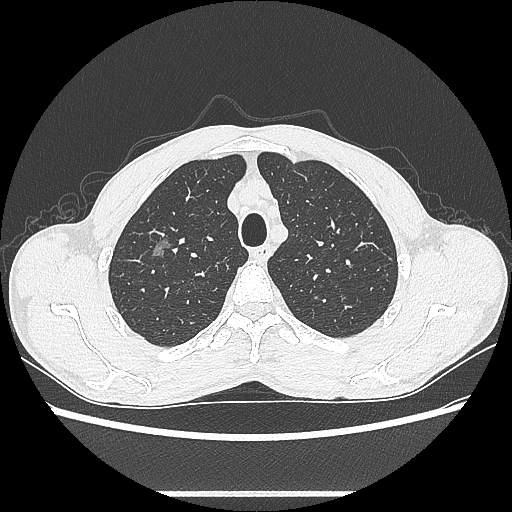
Chest CT, one axial slice. Slice 479 of 601 in the series (ordered by position). 100 kVp. Lung window (W 1500 / L -600 HU). 0.62 mm slice thickness. 512 × 512 image matrix. Male patient, age 54 years. Case-level facts recorded for this patient, not image findings: clinical TNM (as recorded): T1a N0 M0.
Outlined on this slice (bounding box drawn by a radiologist):
- lung tumour (recorded histology: adenocarcinoma): bounding box (x1, y1, x2, y2) in pixels: (145, 232, 175, 268)